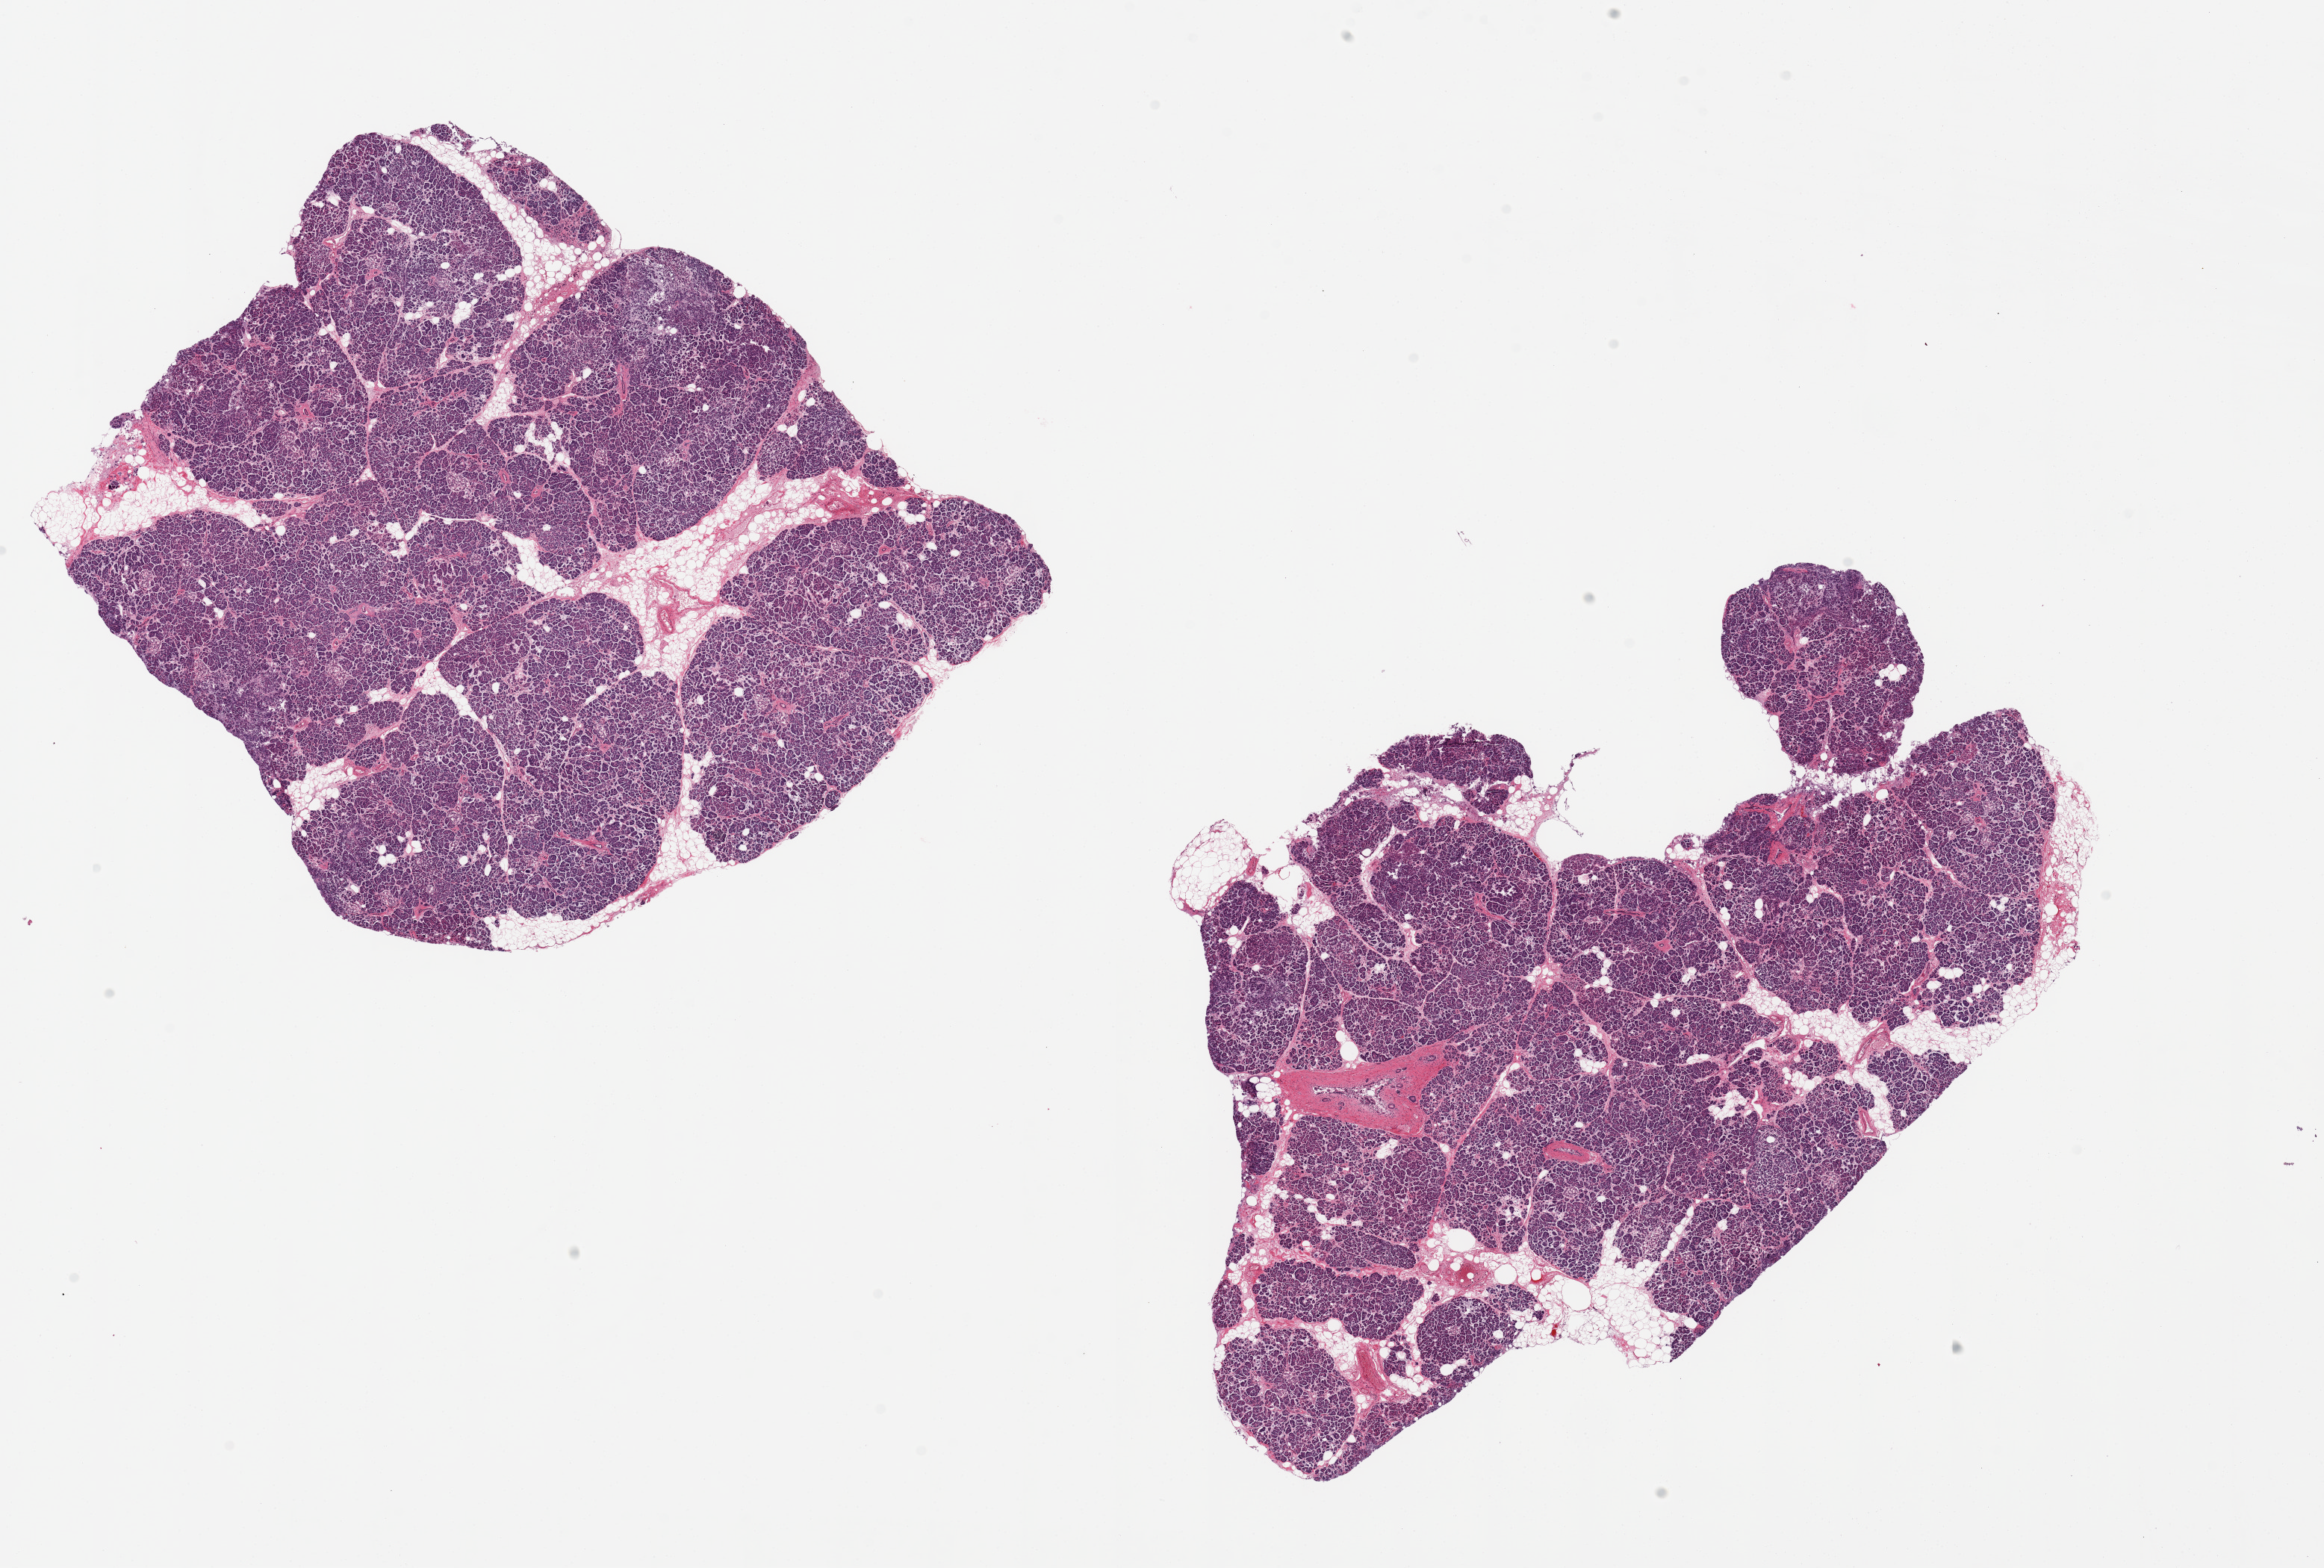
Digitized haematoxylin and eosin-stained section, whole scanned area (about 24.6 x 16.6 mm) shown as a low-resolution overview; PAXgene-fixed, paraffin-embedded tissue; section of pancreas (target tissue); tissue donor sample. Donor sex: male.
Pathologist's review note for this sample: 2 pieces; 9x8 & 11x7.5mm; moderate-severe saponification; Islets poorly seen; a few.